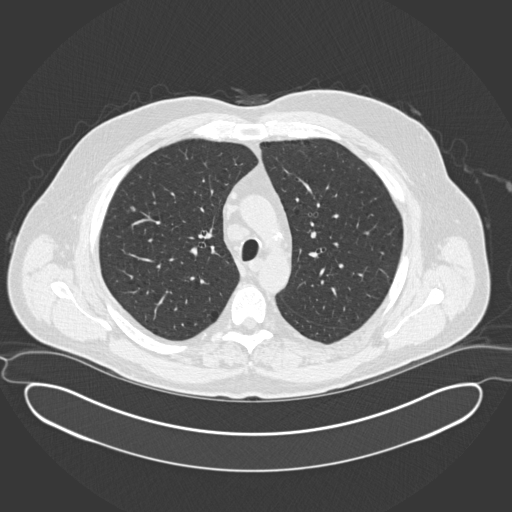
Low-dose screening chest CT, one axial slice; position 119 of 169 along the scan axis; 120 kVp; lung window (W 1500 / L -600 HU); 512 × 512 image matrix, field of view 446 × 446 mm.
Annotated regions visible in this slice (expert manual segmentation):
- lesion 1 (tumor, upper lobe of right lung): box from (x=131, y=206) to (x=136, y=211) px